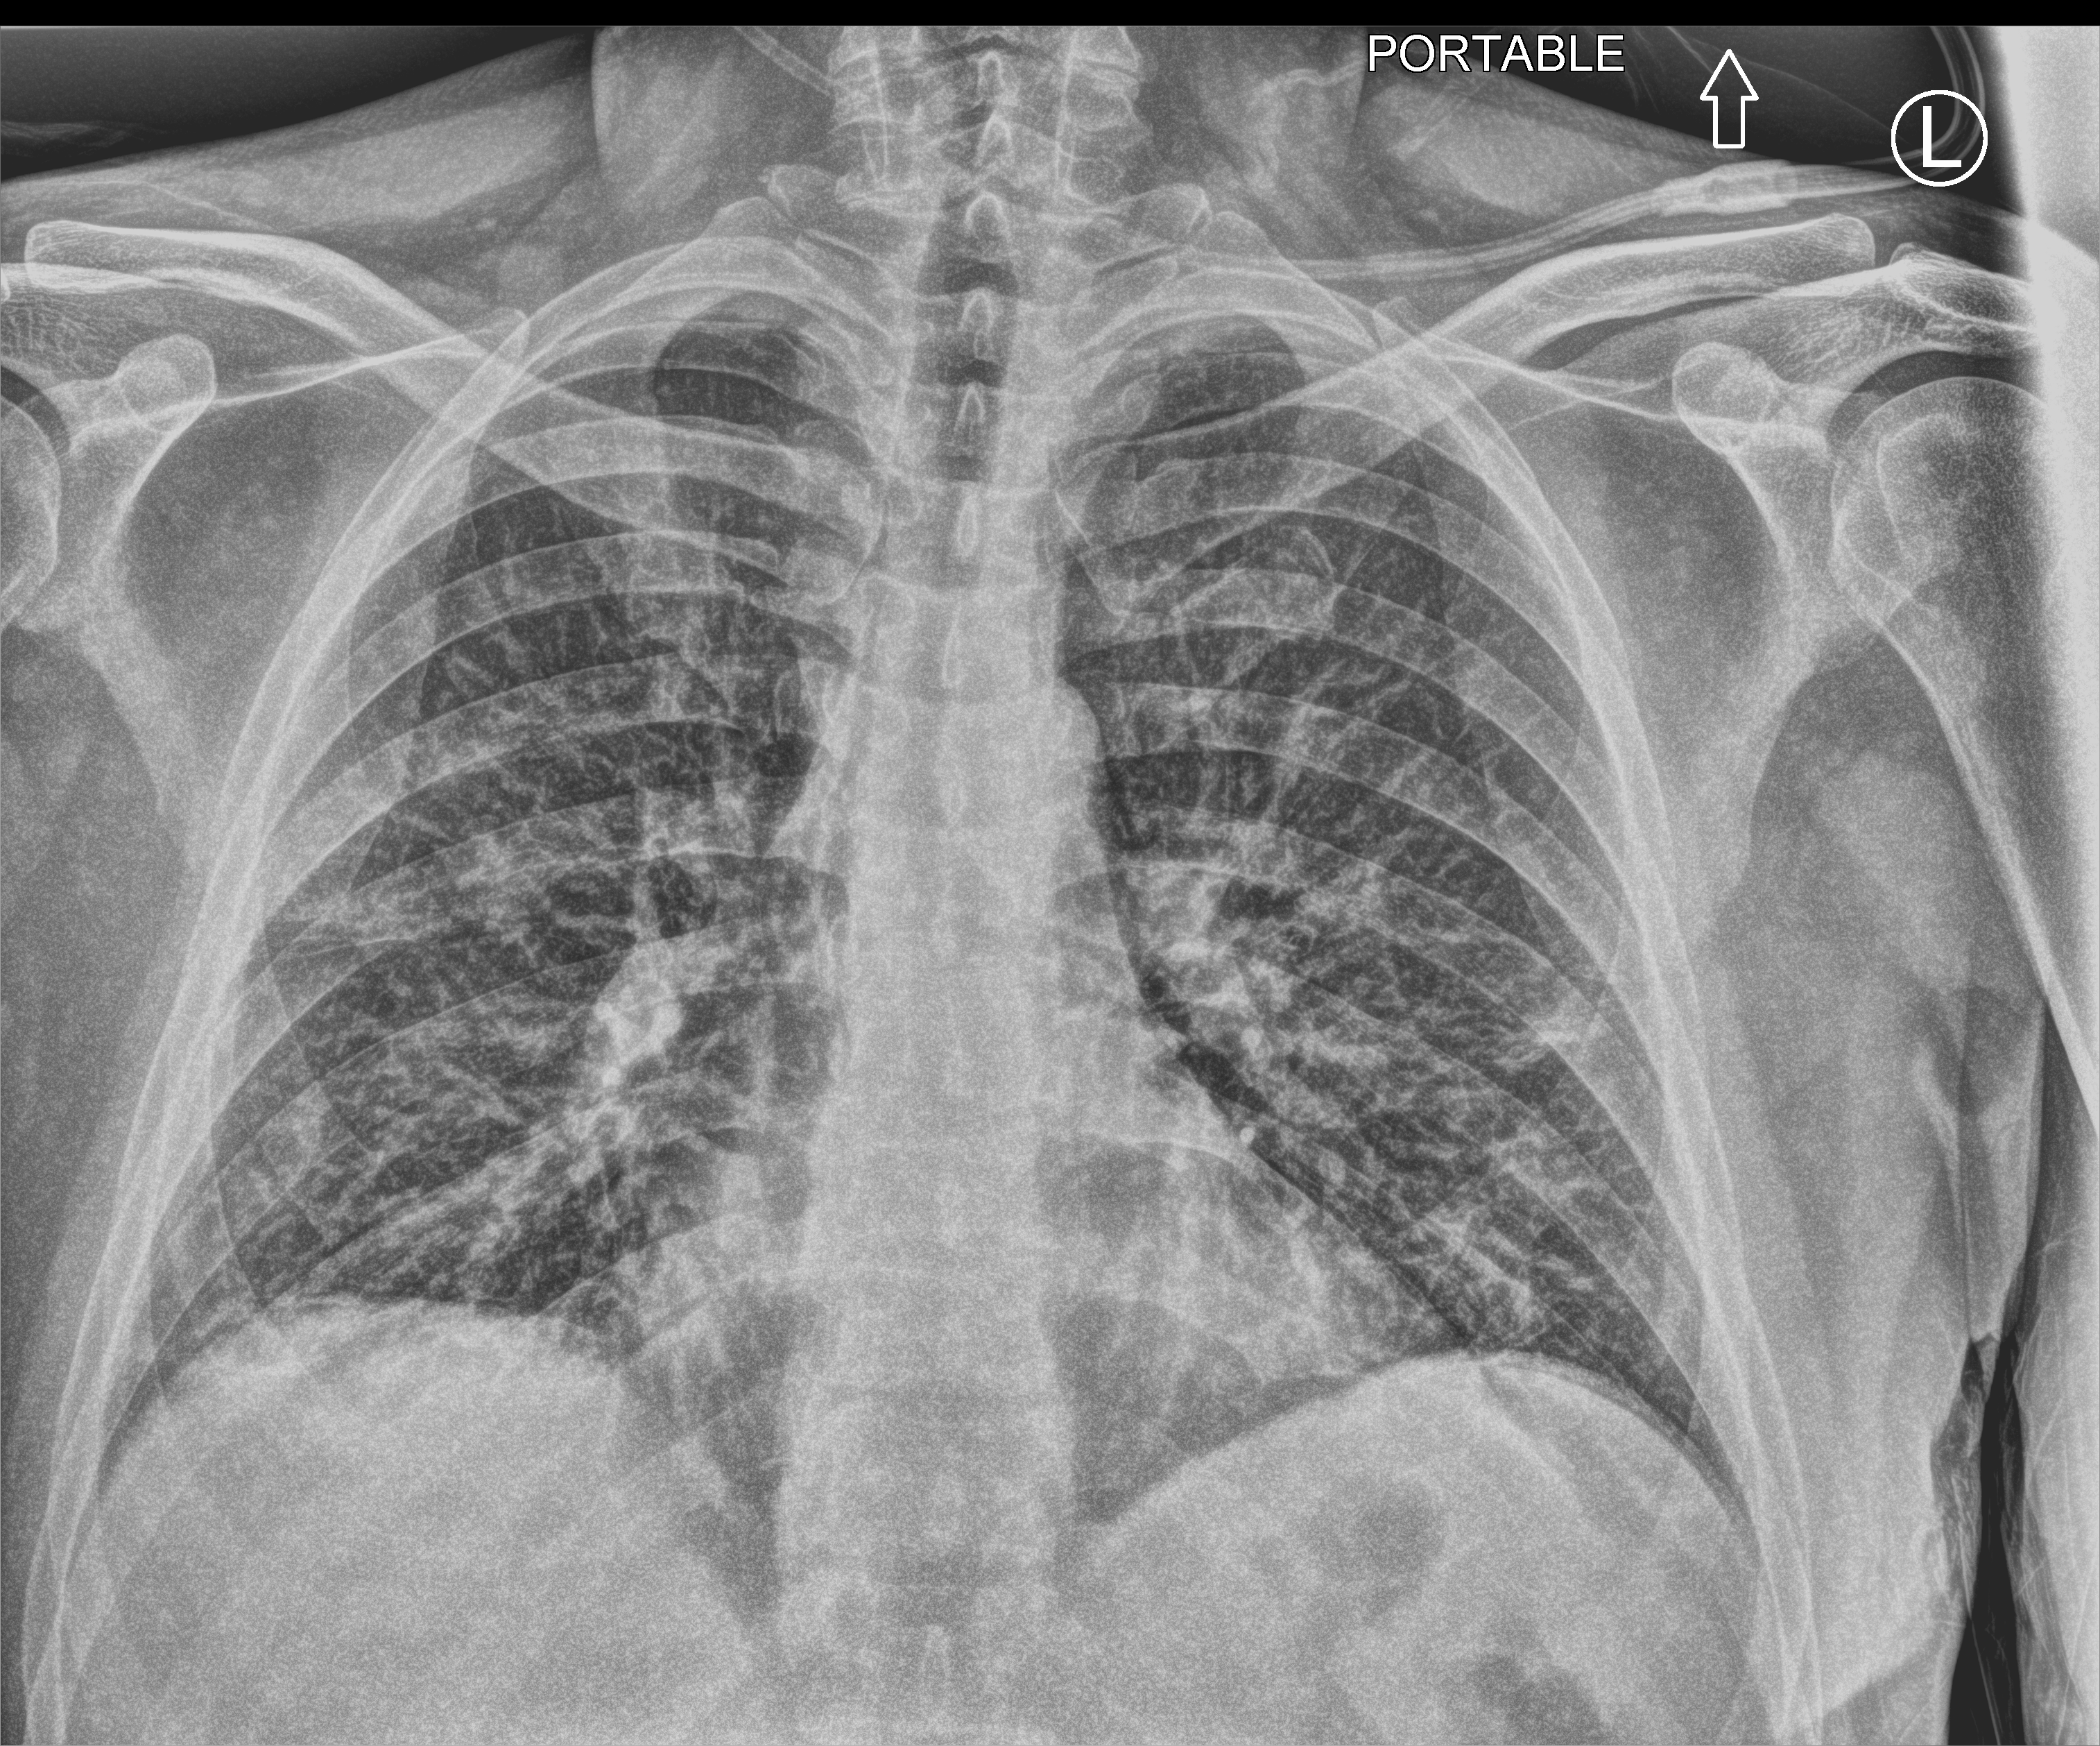
Chest X-ray (portable), anteroposterior (AP) projection. Patient hospitalised with COVID-19; male, aged 60–74 years.
Hospital-stay facts (about this admission, not read from this image; timing relative to this image not recorded):
- mechanically ventilated during this hospital stay: no
- admitted to intensive care during this hospital stay: no
- other chronic lung disease (admission record): no